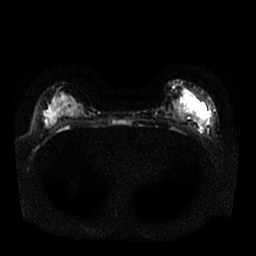
Breast MRI, one axial slice. Slice 10 of 25 in the series (ordered by position). Diffusion-weighted series; image 2 of 4 stored at this slice position (different b-values; order by instance number). 1.5 T. 4 mm slice thickness. 256 × 256 image matrix, field of view 340 × 340 mm. Female patient.
Outlined on this slice (manually delineated by an expert):
- tumour on diffusion-weighted imaging: bounding box <202,108,206,115> (left, top, right, bottom; pixels)